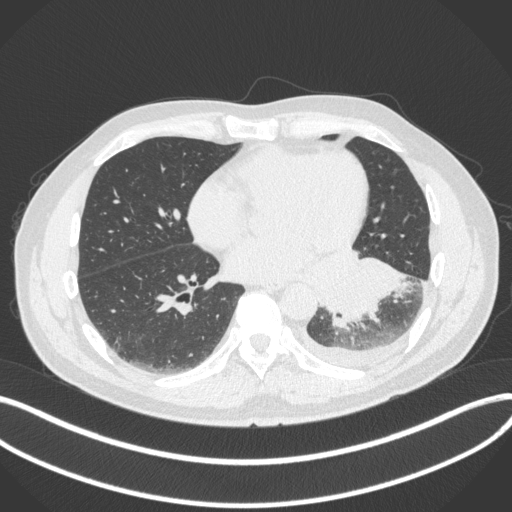
Chest CT, one axial slice. Position 145 of 350 along the scan axis. Lung window (W 1500 / L -600 HU). 1 mm slice thickness. 512 × 512 image matrix. Patient: male, 58 years. From the clinical record (not read from this slice): clinical TNM (as recorded): T3 N1 M1b; histopathological grade: G3.
Outlined on this slice (rectangle marked by the reading radiologist):
- lung tumour (recorded histology: small cell carcinoma): box from (x=334, y=247) to (x=408, y=332) px